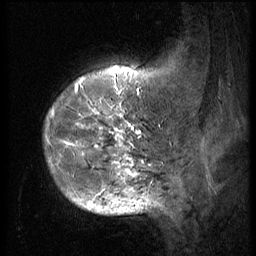
Breast MRI (dynamic contrast-enhanced), one sagittal slice; position 12 of 56 along the scan axis; 3 images stored at this slice position (order not interpretable as contrast timing); 1.5 T; TE 4.2 ms, TR 9 ms; 256 × 256 image matrix, field of view 180 × 180 mm. Patient: female, 49 years. From the clinical record (not read from this slice): setting: breast cancer imaged before/during neoadjuvant chemotherapy; receptor status: HER2-positive.
Outlined on this slice (semi-automatic segmentation, software-assisted and operator-edited):
- analysis volume of interest (the breast-tissue region the enhancement analysis was run in; not a lesion): bounding box <43,79,152,203> (left, top, right, bottom; pixels)
- tumour enhancement mask (voxels above the 140 % enhancement threshold inside the analysis volume of interest): <48,79,144,203>